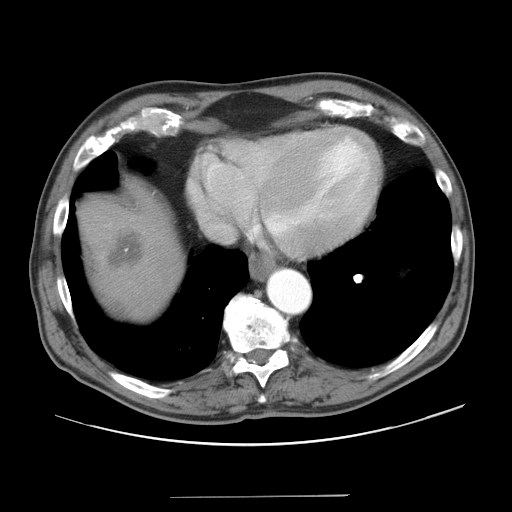
Contrast-enhanced abdominal CT, one axial slice. Position 38 of 41 along the scan axis. Intravenous contrast given. Soft-tissue window (W 400 / L 40 HU). 5 mm slice thickness. 512 × 512 image matrix. Male patient, age 75 years. From the clinical record (not read from this slice): diagnosis: colorectal cancer liver metastases, imaged before liver resection; multiple liver metastases: no; largest metastasis: 5.2 cm; disease in both lobes: no.
Outlined on this slice (manually delineated by an expert):
- liver: bounding box (x1, y1, x2, y2) in pixels: (83, 200, 176, 307)
- planned liver remnant (the part of the liver to remain after resection): (138, 271, 174, 307)
- liver metastasis: (109, 235, 144, 269)